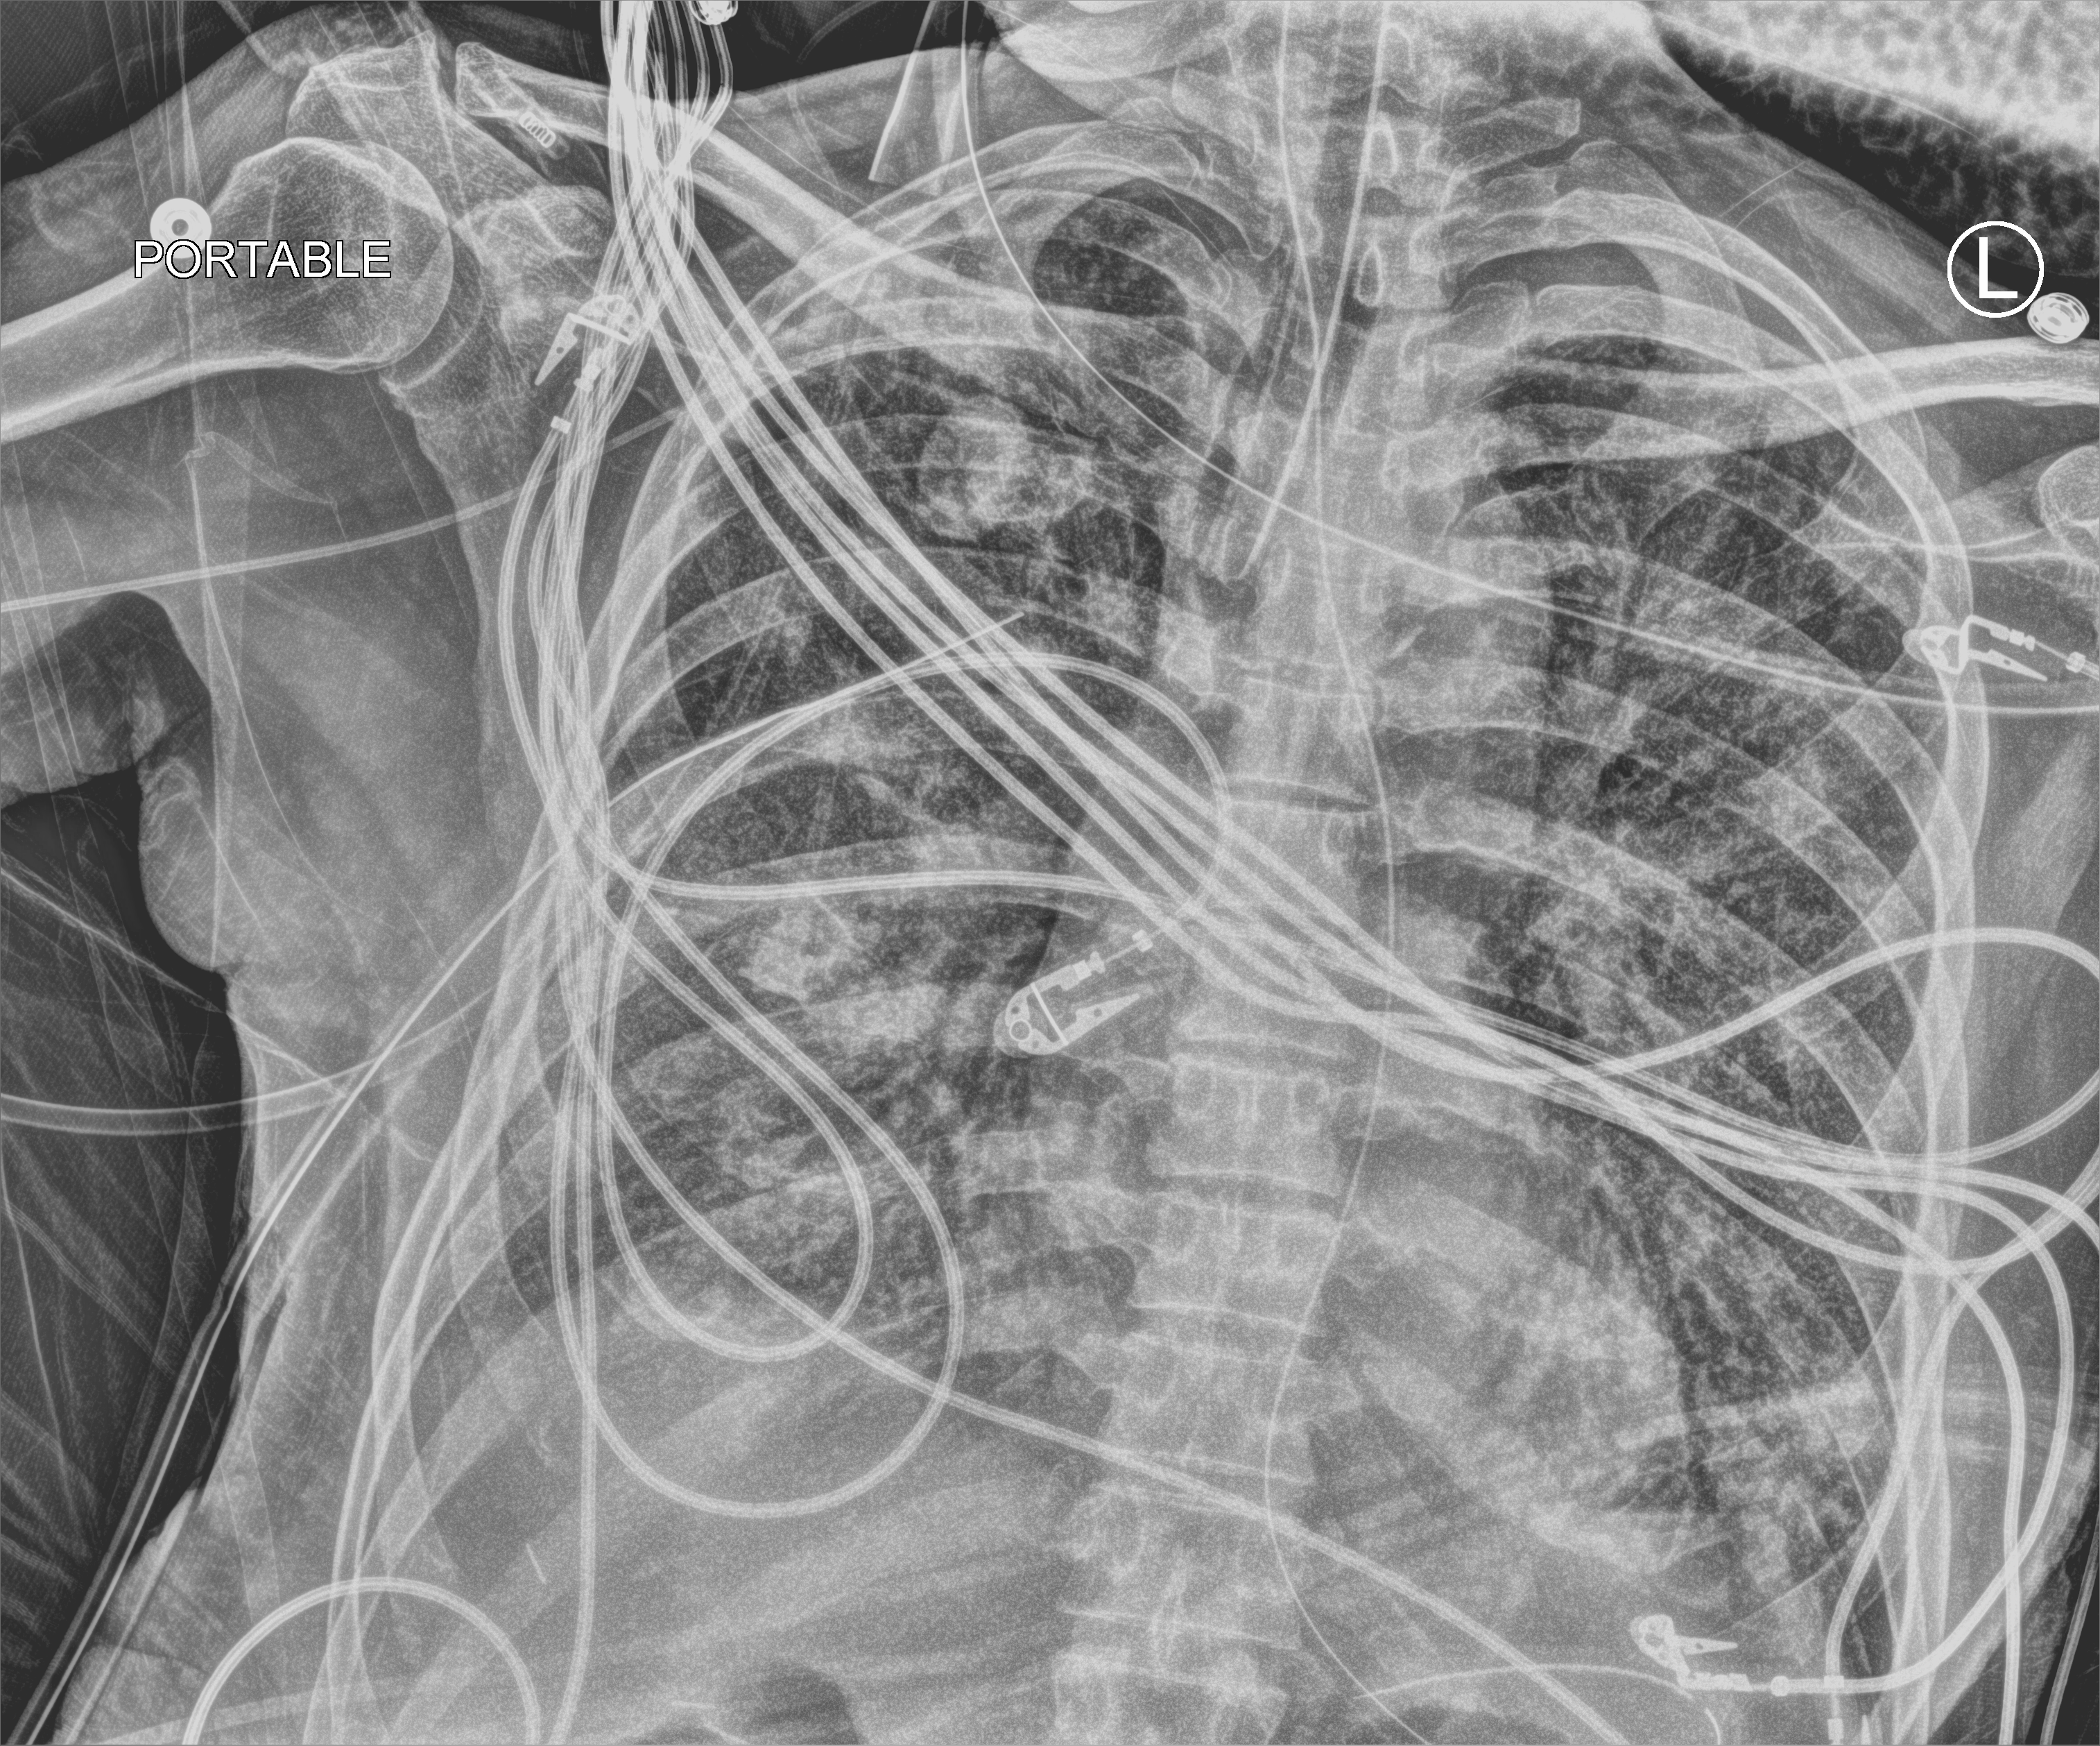
Chest X-ray (portable), anteroposterior (AP) projection. Patient hospitalised with COVID-19; male, aged 60–74 years.
Admission-level facts for this patient (not findings on this image; timing relative to this image not recorded): mechanically ventilated during this hospital stay: yes.